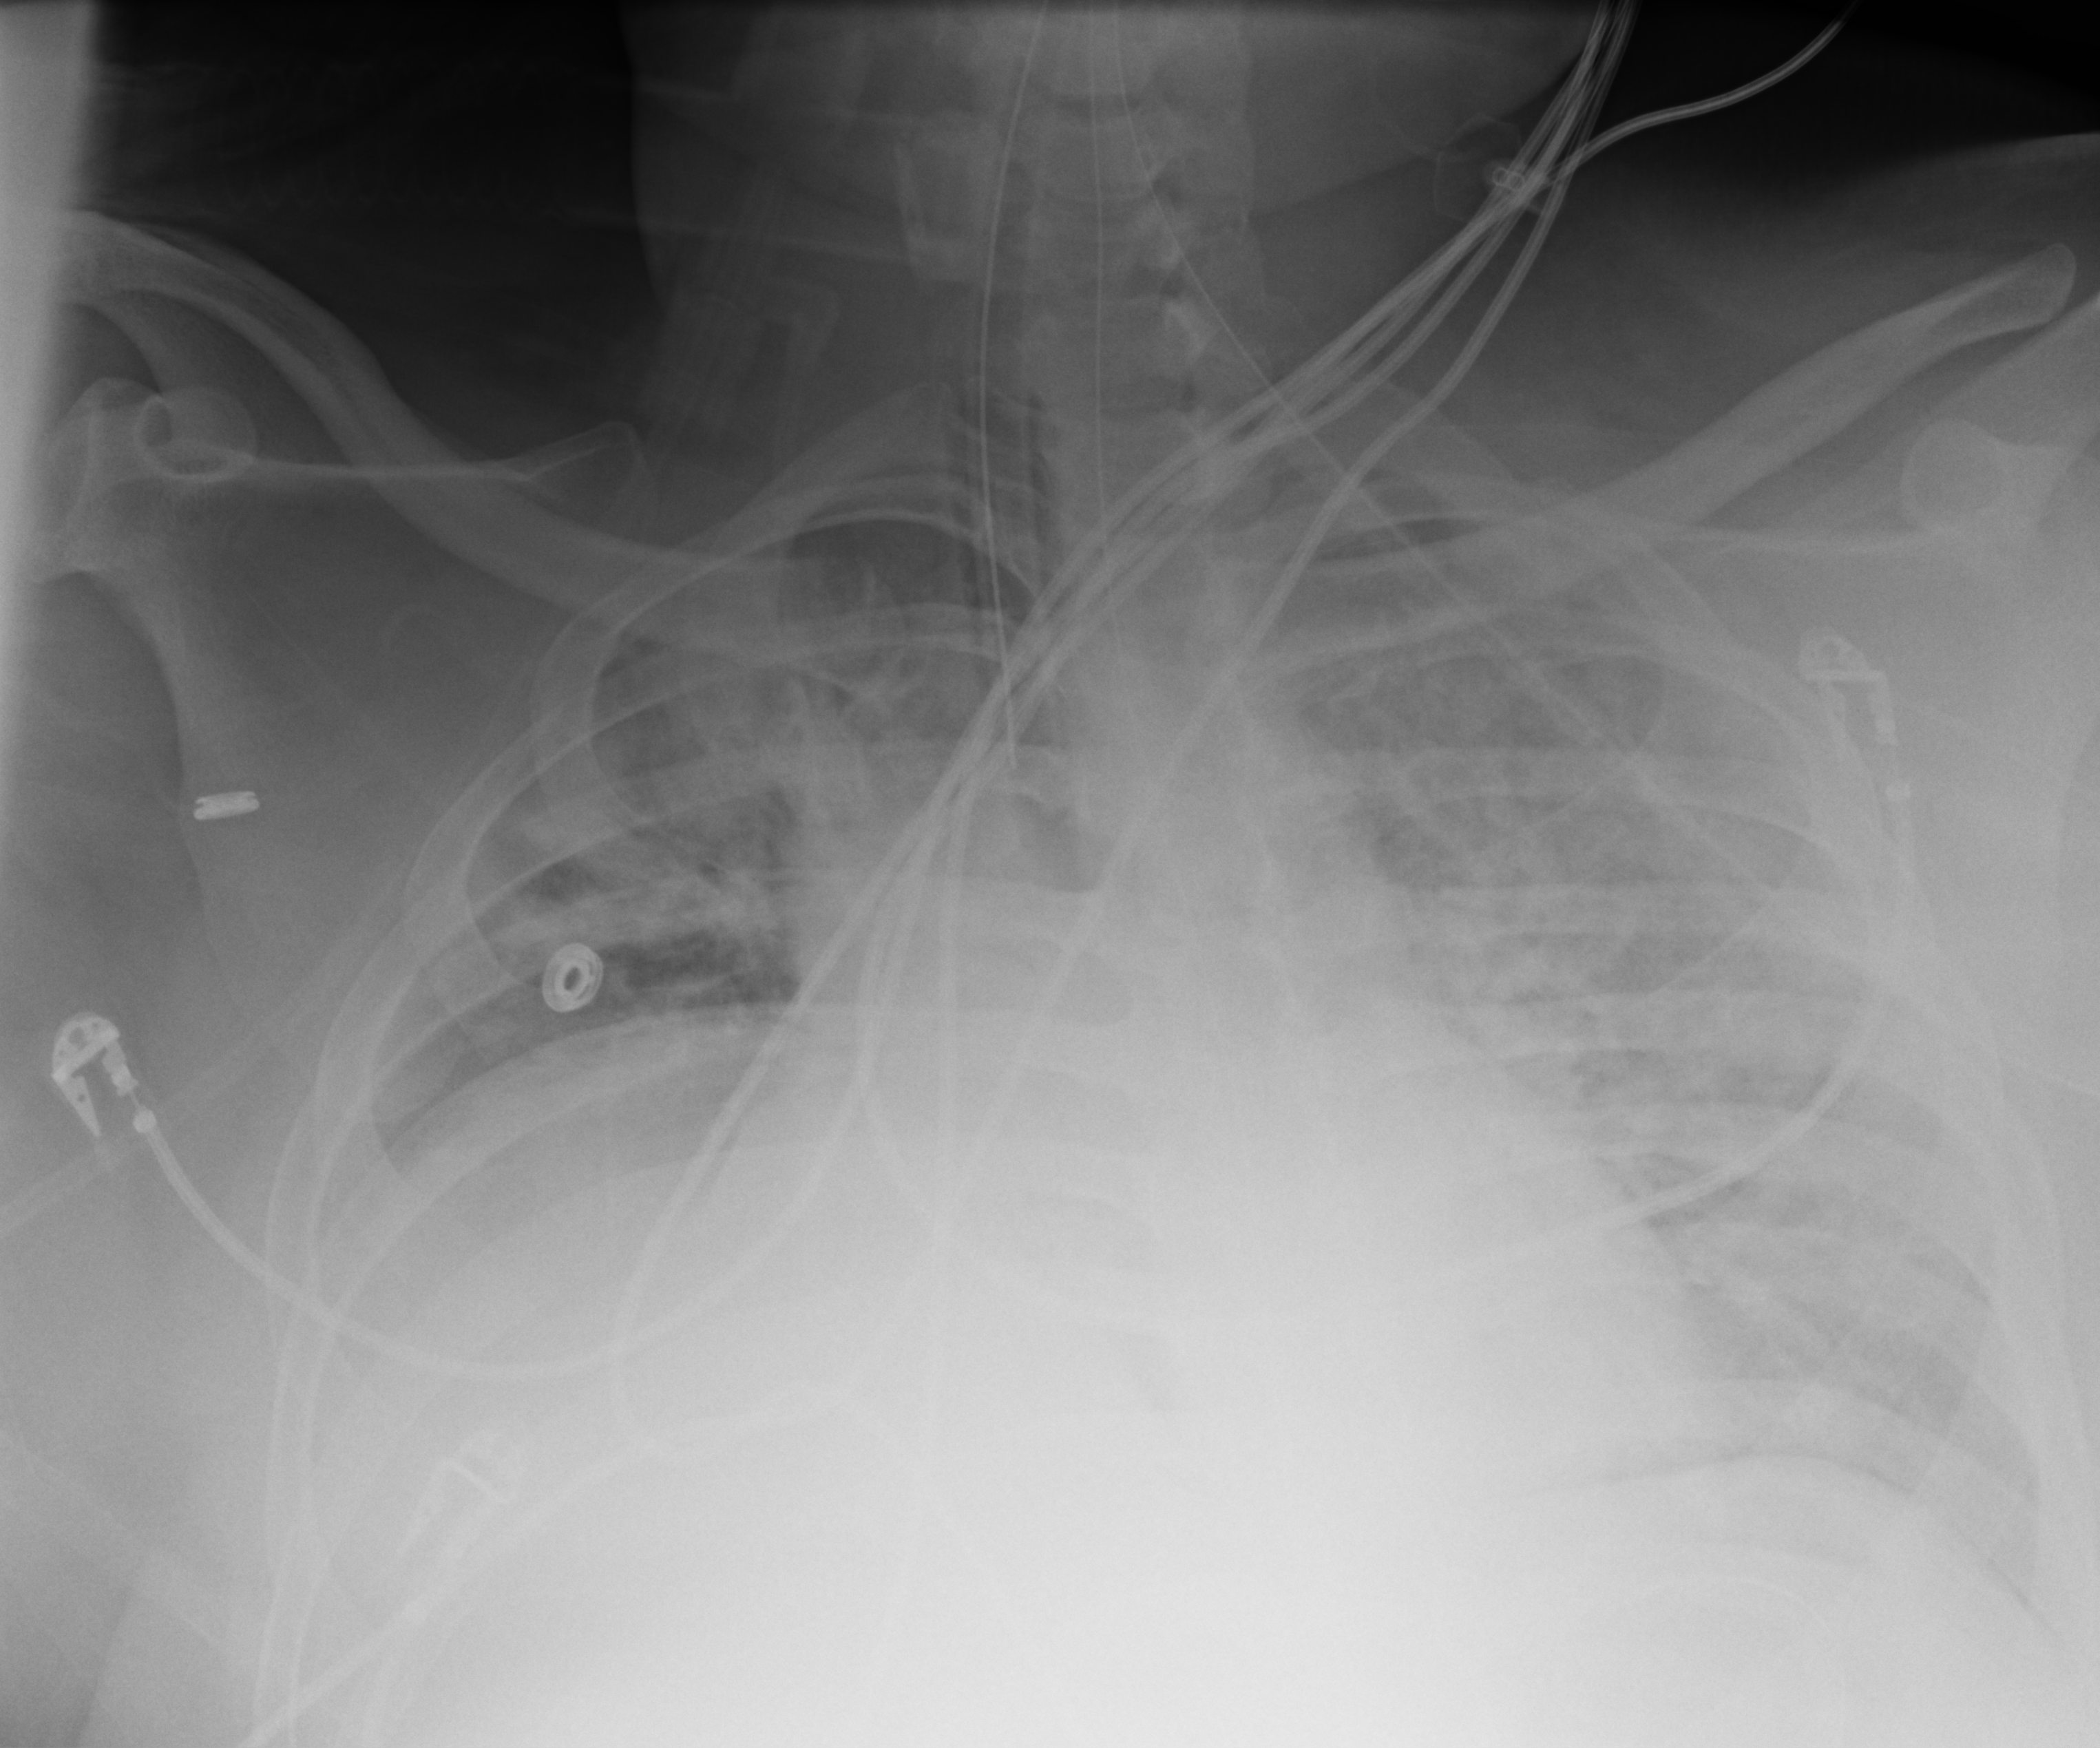
Chest X-ray (portable); anteroposterior (AP) projection. Patient hospitalised with COVID-19; male, aged 18–59 years.
Admission-level facts for this patient (not findings on this image; timing relative to this image not recorded): mechanically ventilated during this hospital stay: yes.